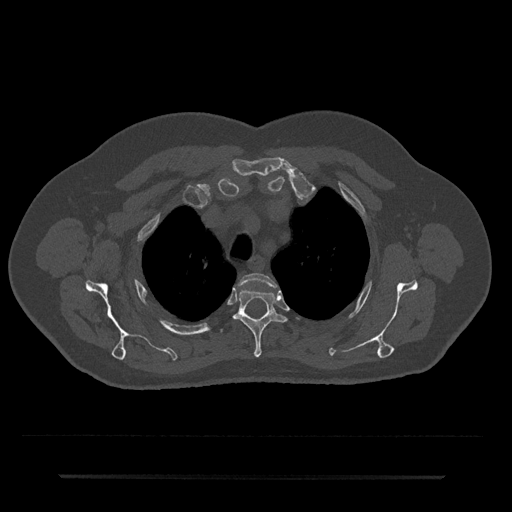
CT including the spine, one axial slice. Slice 569 of 797 in the series (ordered by position). Bone window (W 1800 / L 400 HU). 512 × 512 image matrix, field of view 437 × 437 mm. Patient: male, 69 years. Case-level facts recorded for this patient, not image findings: primary cancer: prostate.
Outlined on this slice (semi-automatic segmentation, software-assisted and operator-edited):
- T2 vertebra: box from (x=239, y=273) to (x=276, y=288) px
- T3 vertebra: (x=233, y=288)–(x=286, y=358)
- T4 vertebra: (x=220, y=329)–(x=223, y=332)